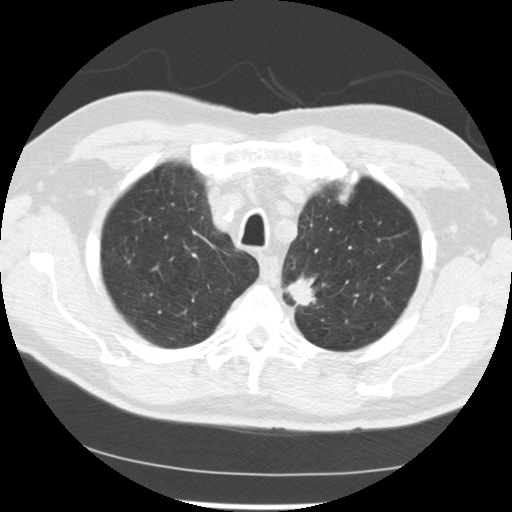
Axial slice from a low-dose chest CT screening exam. First (baseline) screen. Lung window (W 1500 / L -600 HU). 2.5 mm slice thickness. Standard (soft-tissue) reconstruction kernel (STANDARD). Slice 204 of 249 in the series. Male participant, aged 71 years at enrolment. Current smoker at enrolment.
Expert reader's lesion annotation, bounding box (x1, y1, x2, y2) in pixels: (273, 265, 336, 317). The screening reader recorded 2 non-calcified nodules or masses ≥4 mm on this exam (left upper lobe, left upper lobe); which of them this box marks is not recorded.